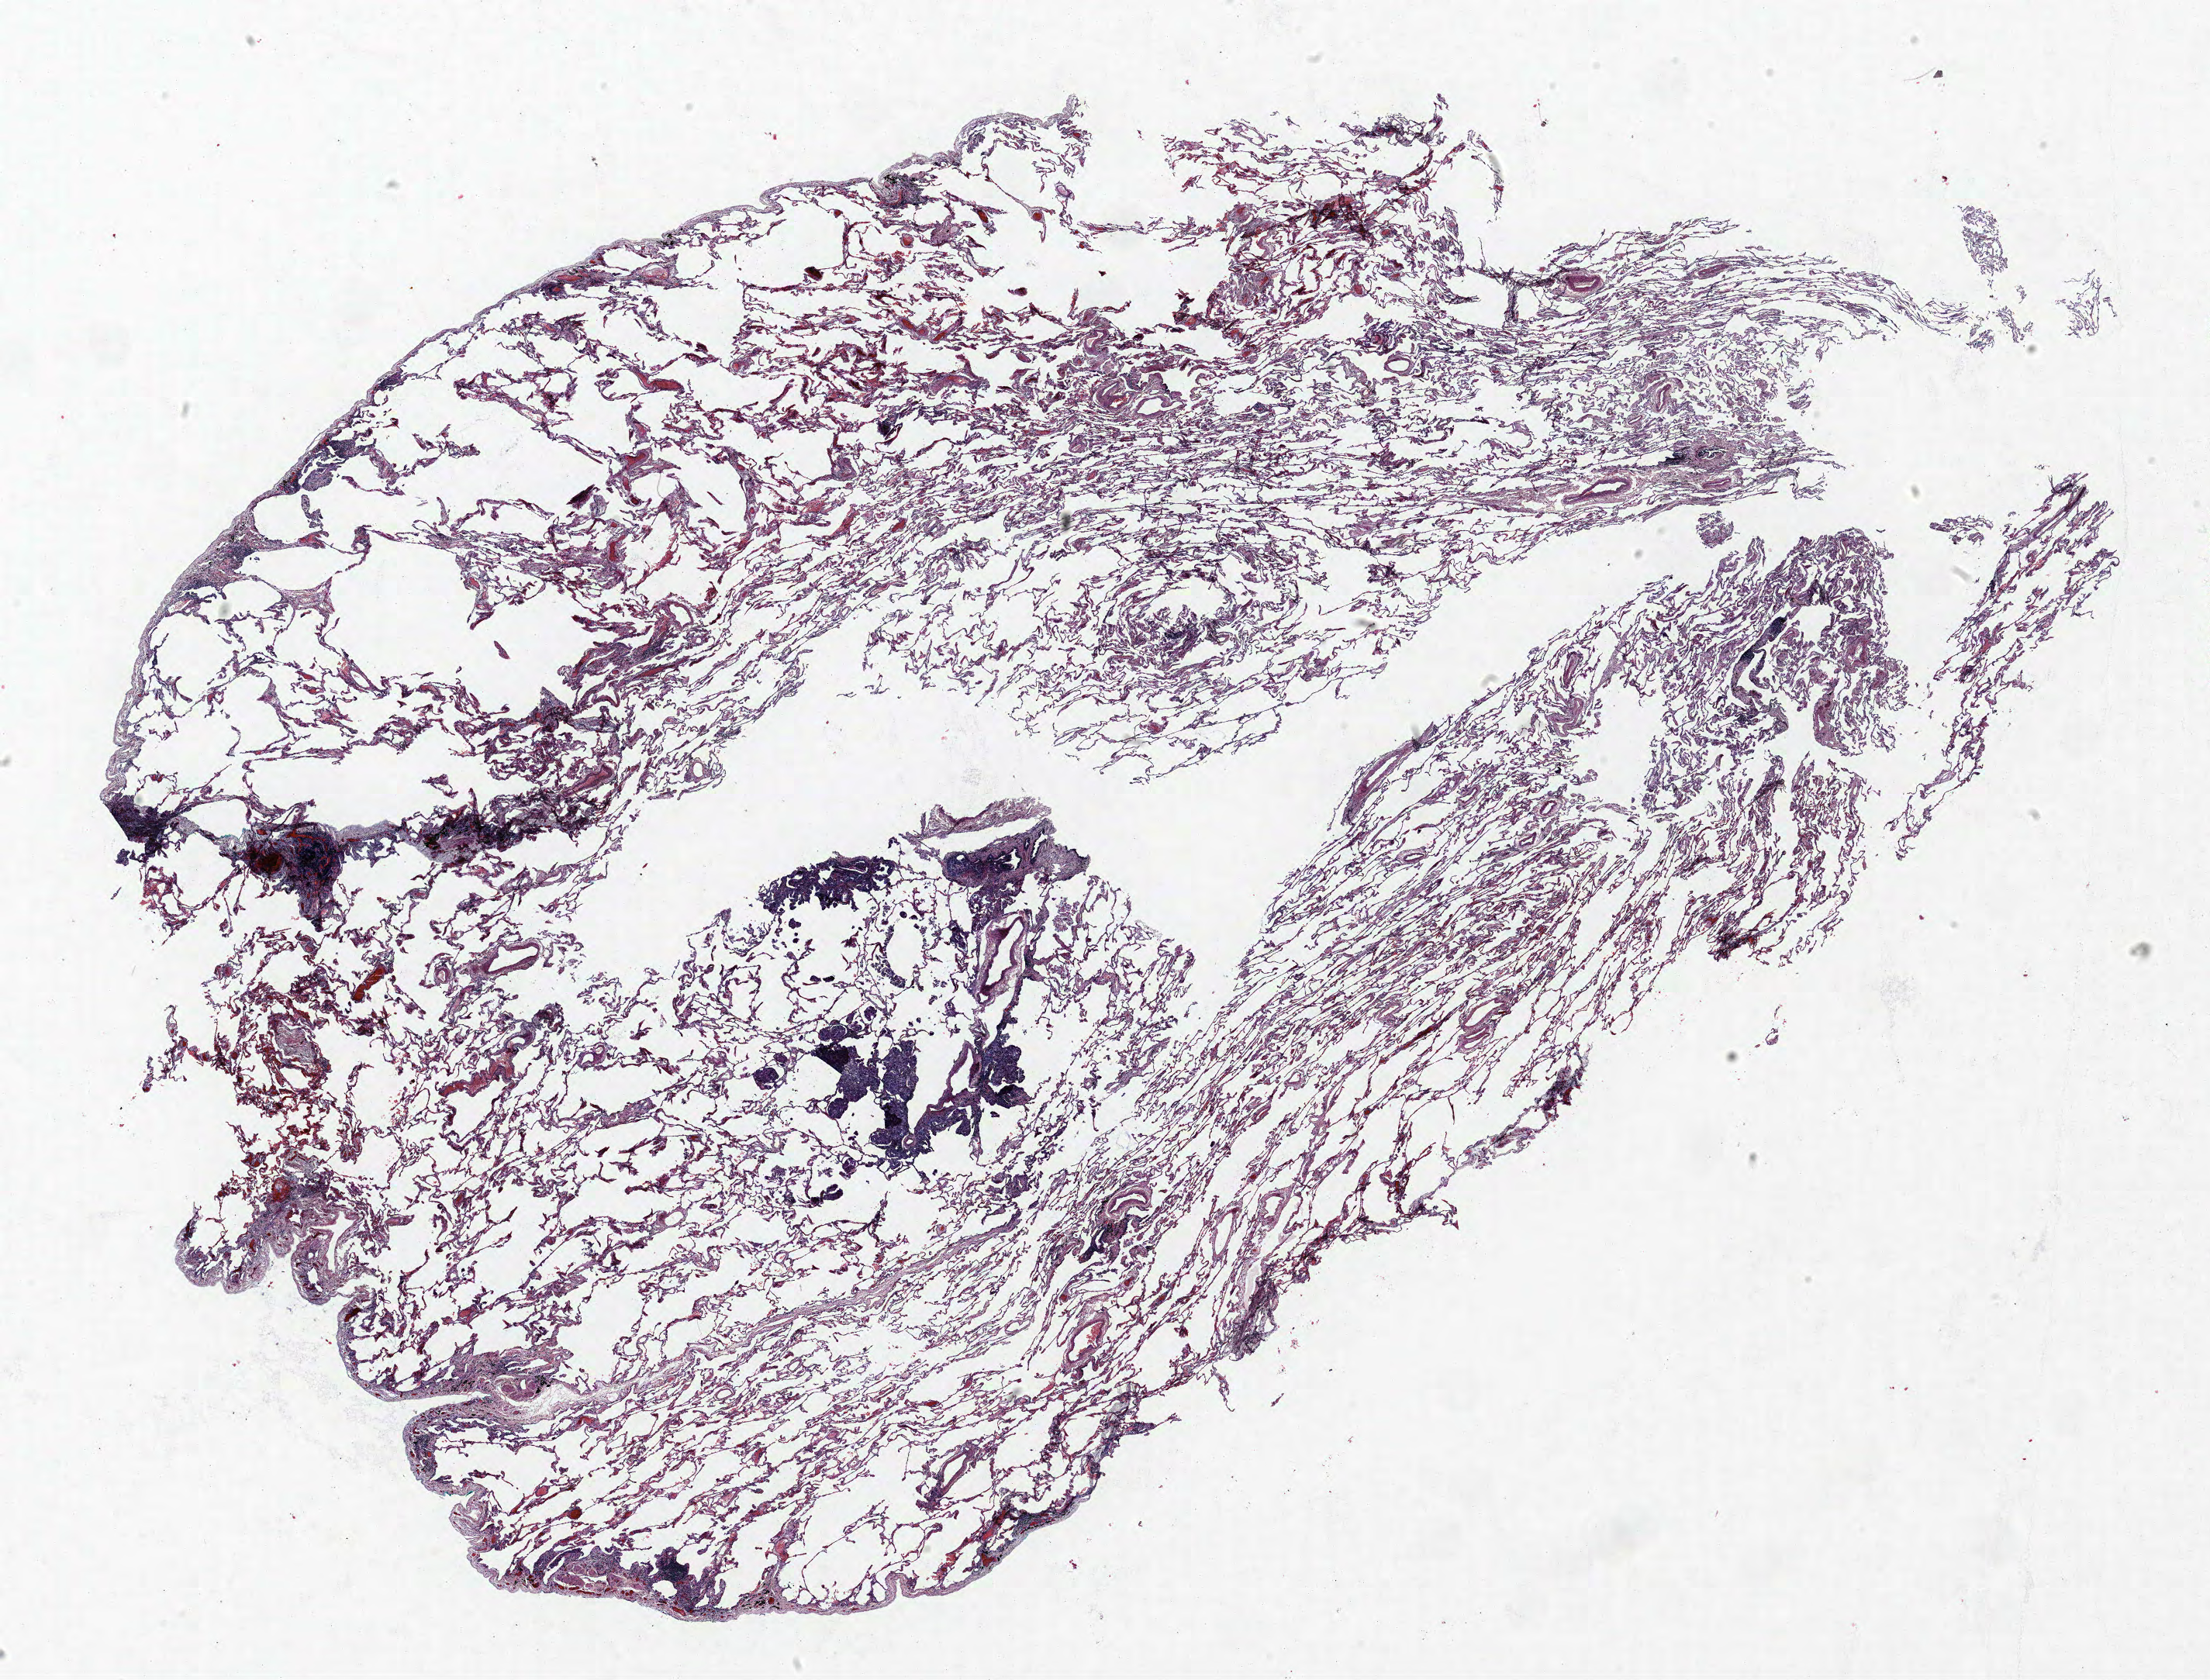
Whole-slide histology image, H&E, a low-resolution overview of the entire scanned area, about 22.8 x 17.3 mm (from a 40x scan); FFPE section; lung. Male, age 70 at enrolment. Former smoker at enrolment. Grade: moderately differentiated (G2).
Participant's lung-cancer diagnosis: Mucin-producing adenocarcinoma (ICD-O-3 8481/3). Primary tumour location (clinical record): left upper lobe. Stage (AJCC 6th edition): IA. ICD-O-3 topography: upper lobe of lung (C34.1). Tumour size (pathology): 20 mm.